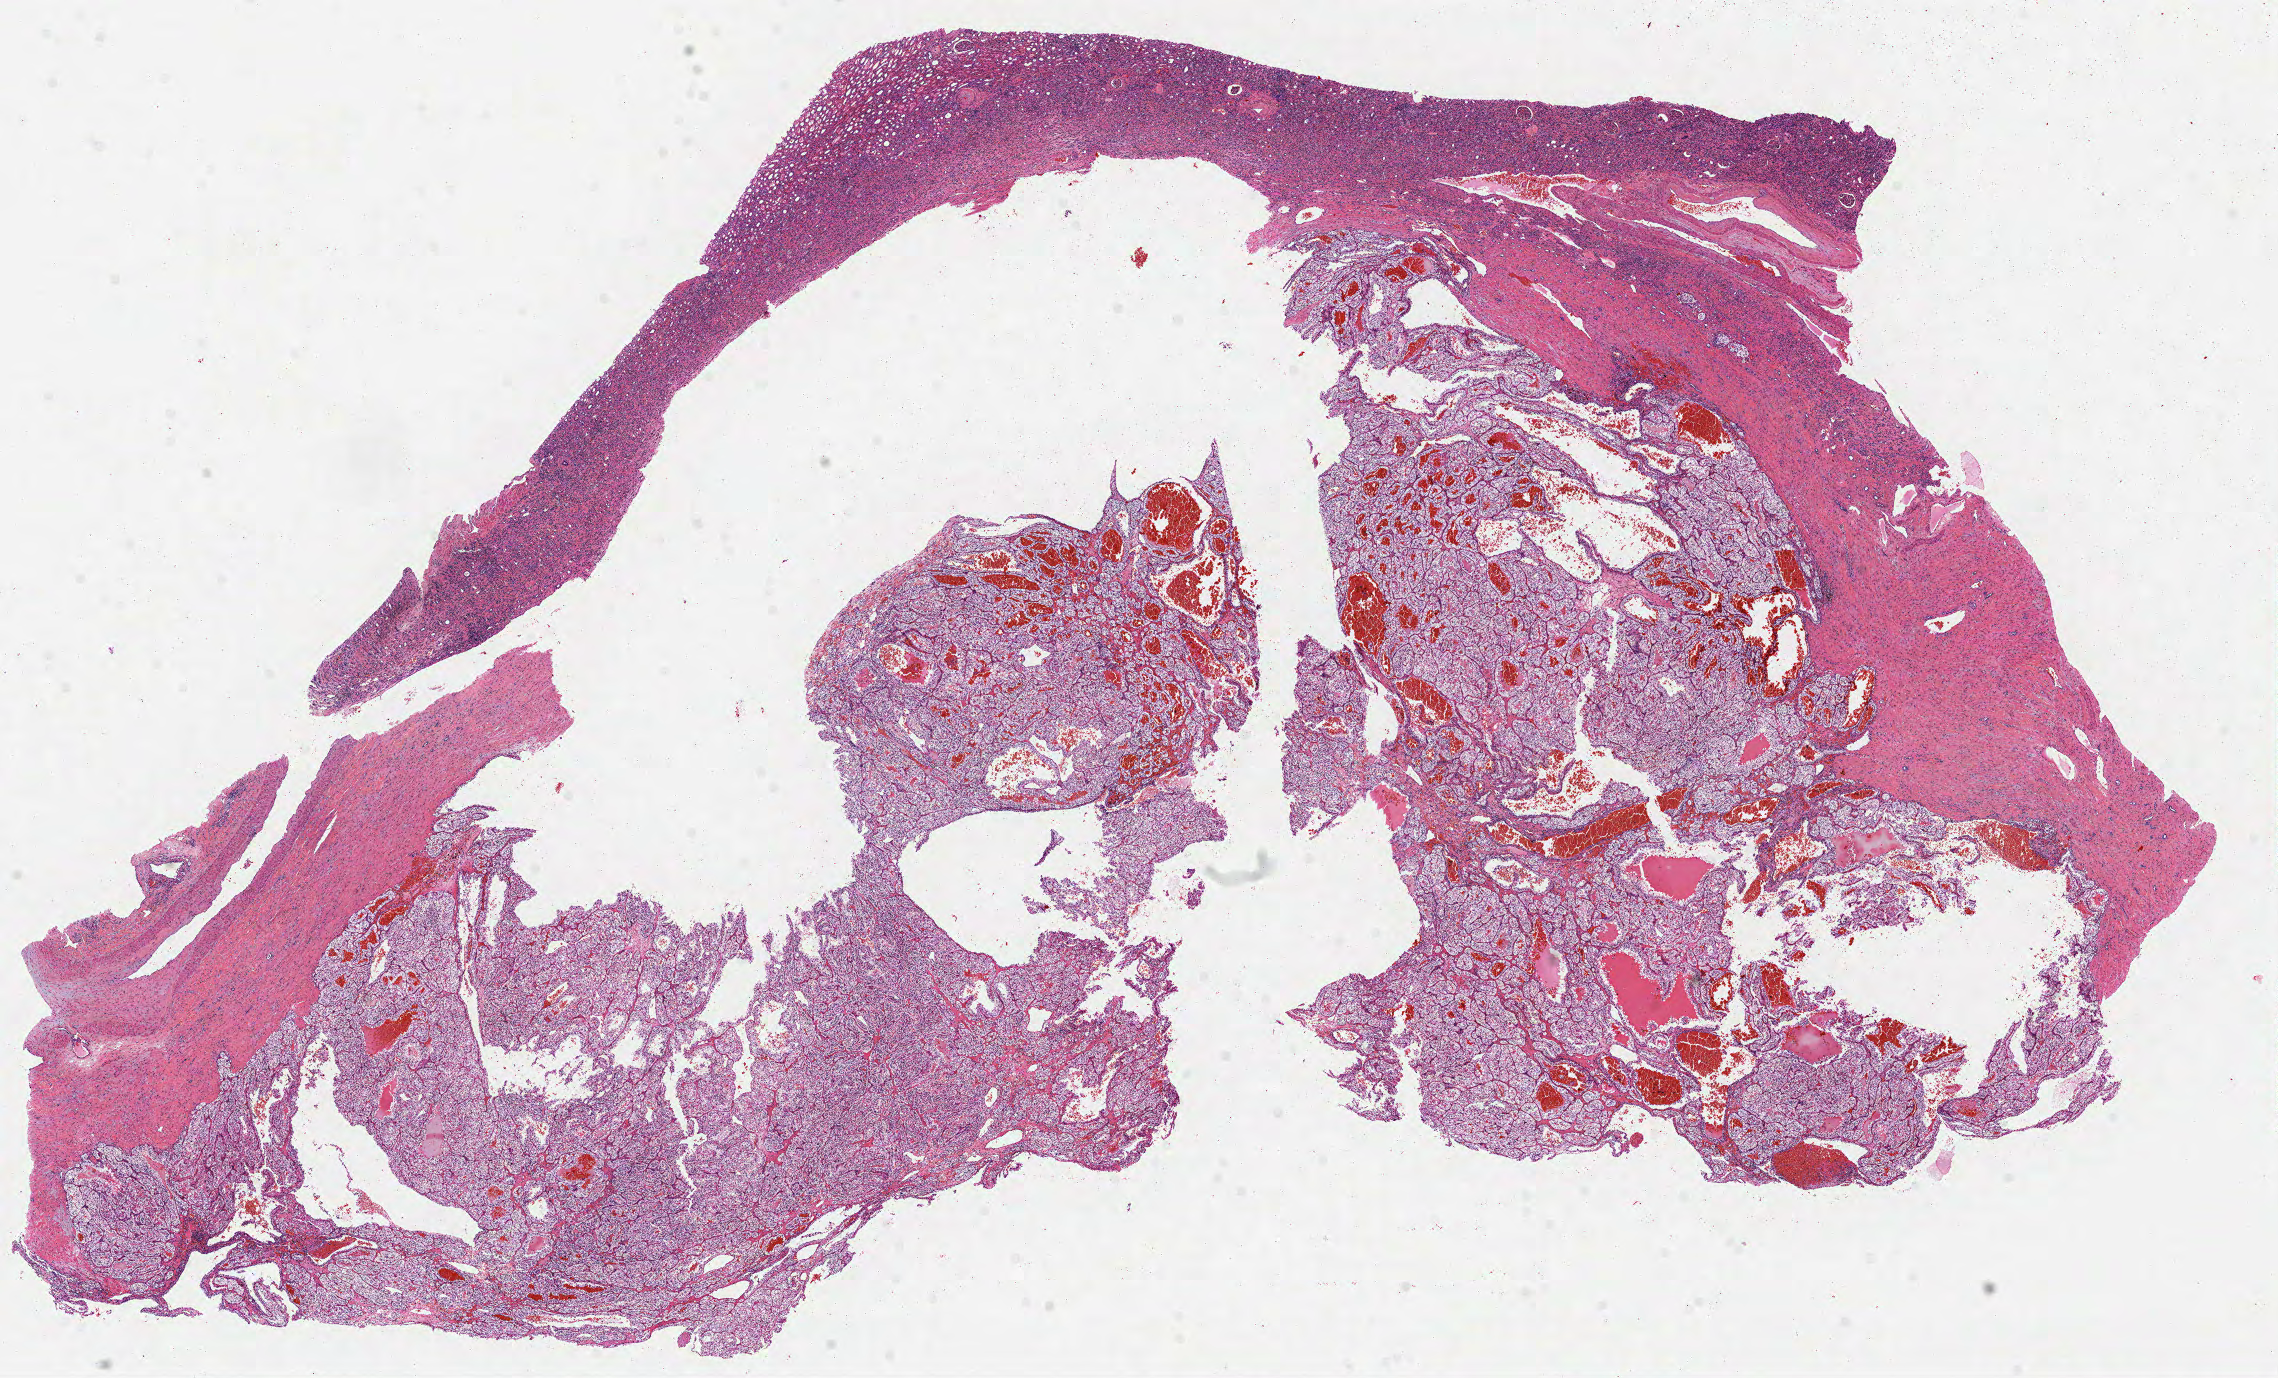
H&E whole-slide image, a low-resolution overview of the entire scanned area, about 18.4 x 11.1 mm (acquisition: 40x scan); formalin-fixed paraffin-embedded (FFPE) diagnostic section; sample: primary tumour, kidney. Male, age 45 years at initial diagnosis. Histologic grade: G2 (moderately differentiated).
AJCC pathologic stage: I. Diagnosis: Clear cell adenocarcinoma, NOS.